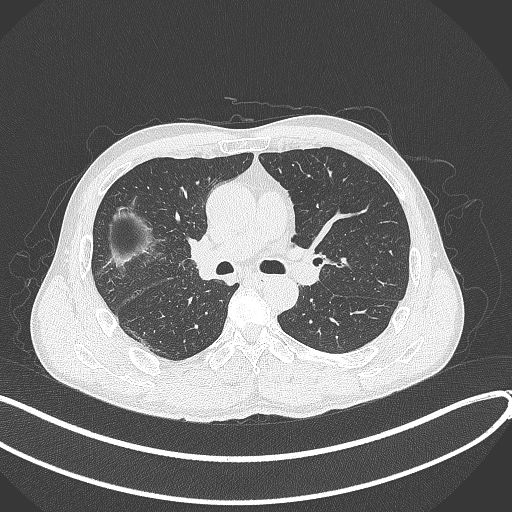
Chest CT, one axial slice. Position 230 of 409 along the scan axis. Reconstruction kernel B70f. Lung window (W 1500 / L -600 HU). 1 mm slice thickness. 512 × 512 image matrix, field of view 400 × 400 mm. Male patient, age 53 years. Case-level facts recorded for this patient, not image findings: clinical TNM (as recorded): T1b N0 M0.
Outlined on this slice (bounding box drawn by a radiologist):
- lung tumour (recorded histology: squamous cell carcinoma): bounding box [x1, y1, x2, y2] px = [183, 231, 229, 295]